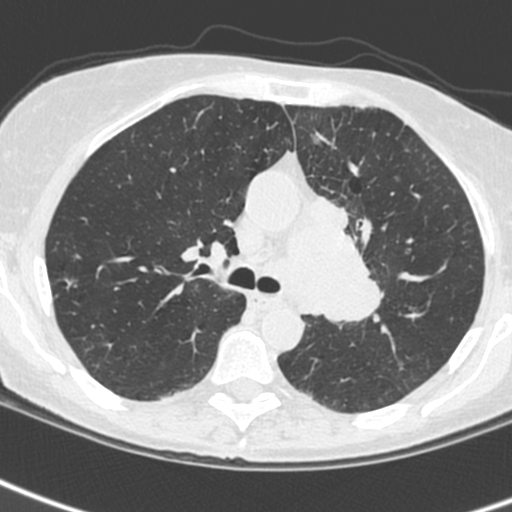
Low-dose screening chest CT, one axial slice; position 161 of 242 along the scan axis; lung window (W 1500 / L -600 HU); 1.3 mm slice thickness; 512 × 512 image matrix, field of view 284 × 284 mm.
Structures marked on this image (manually delineated by an expert):
- lesion 3 (tumor, upper lobe of left lung): bounding box <305,193,384,322> (left, top, right, bottom; pixels)